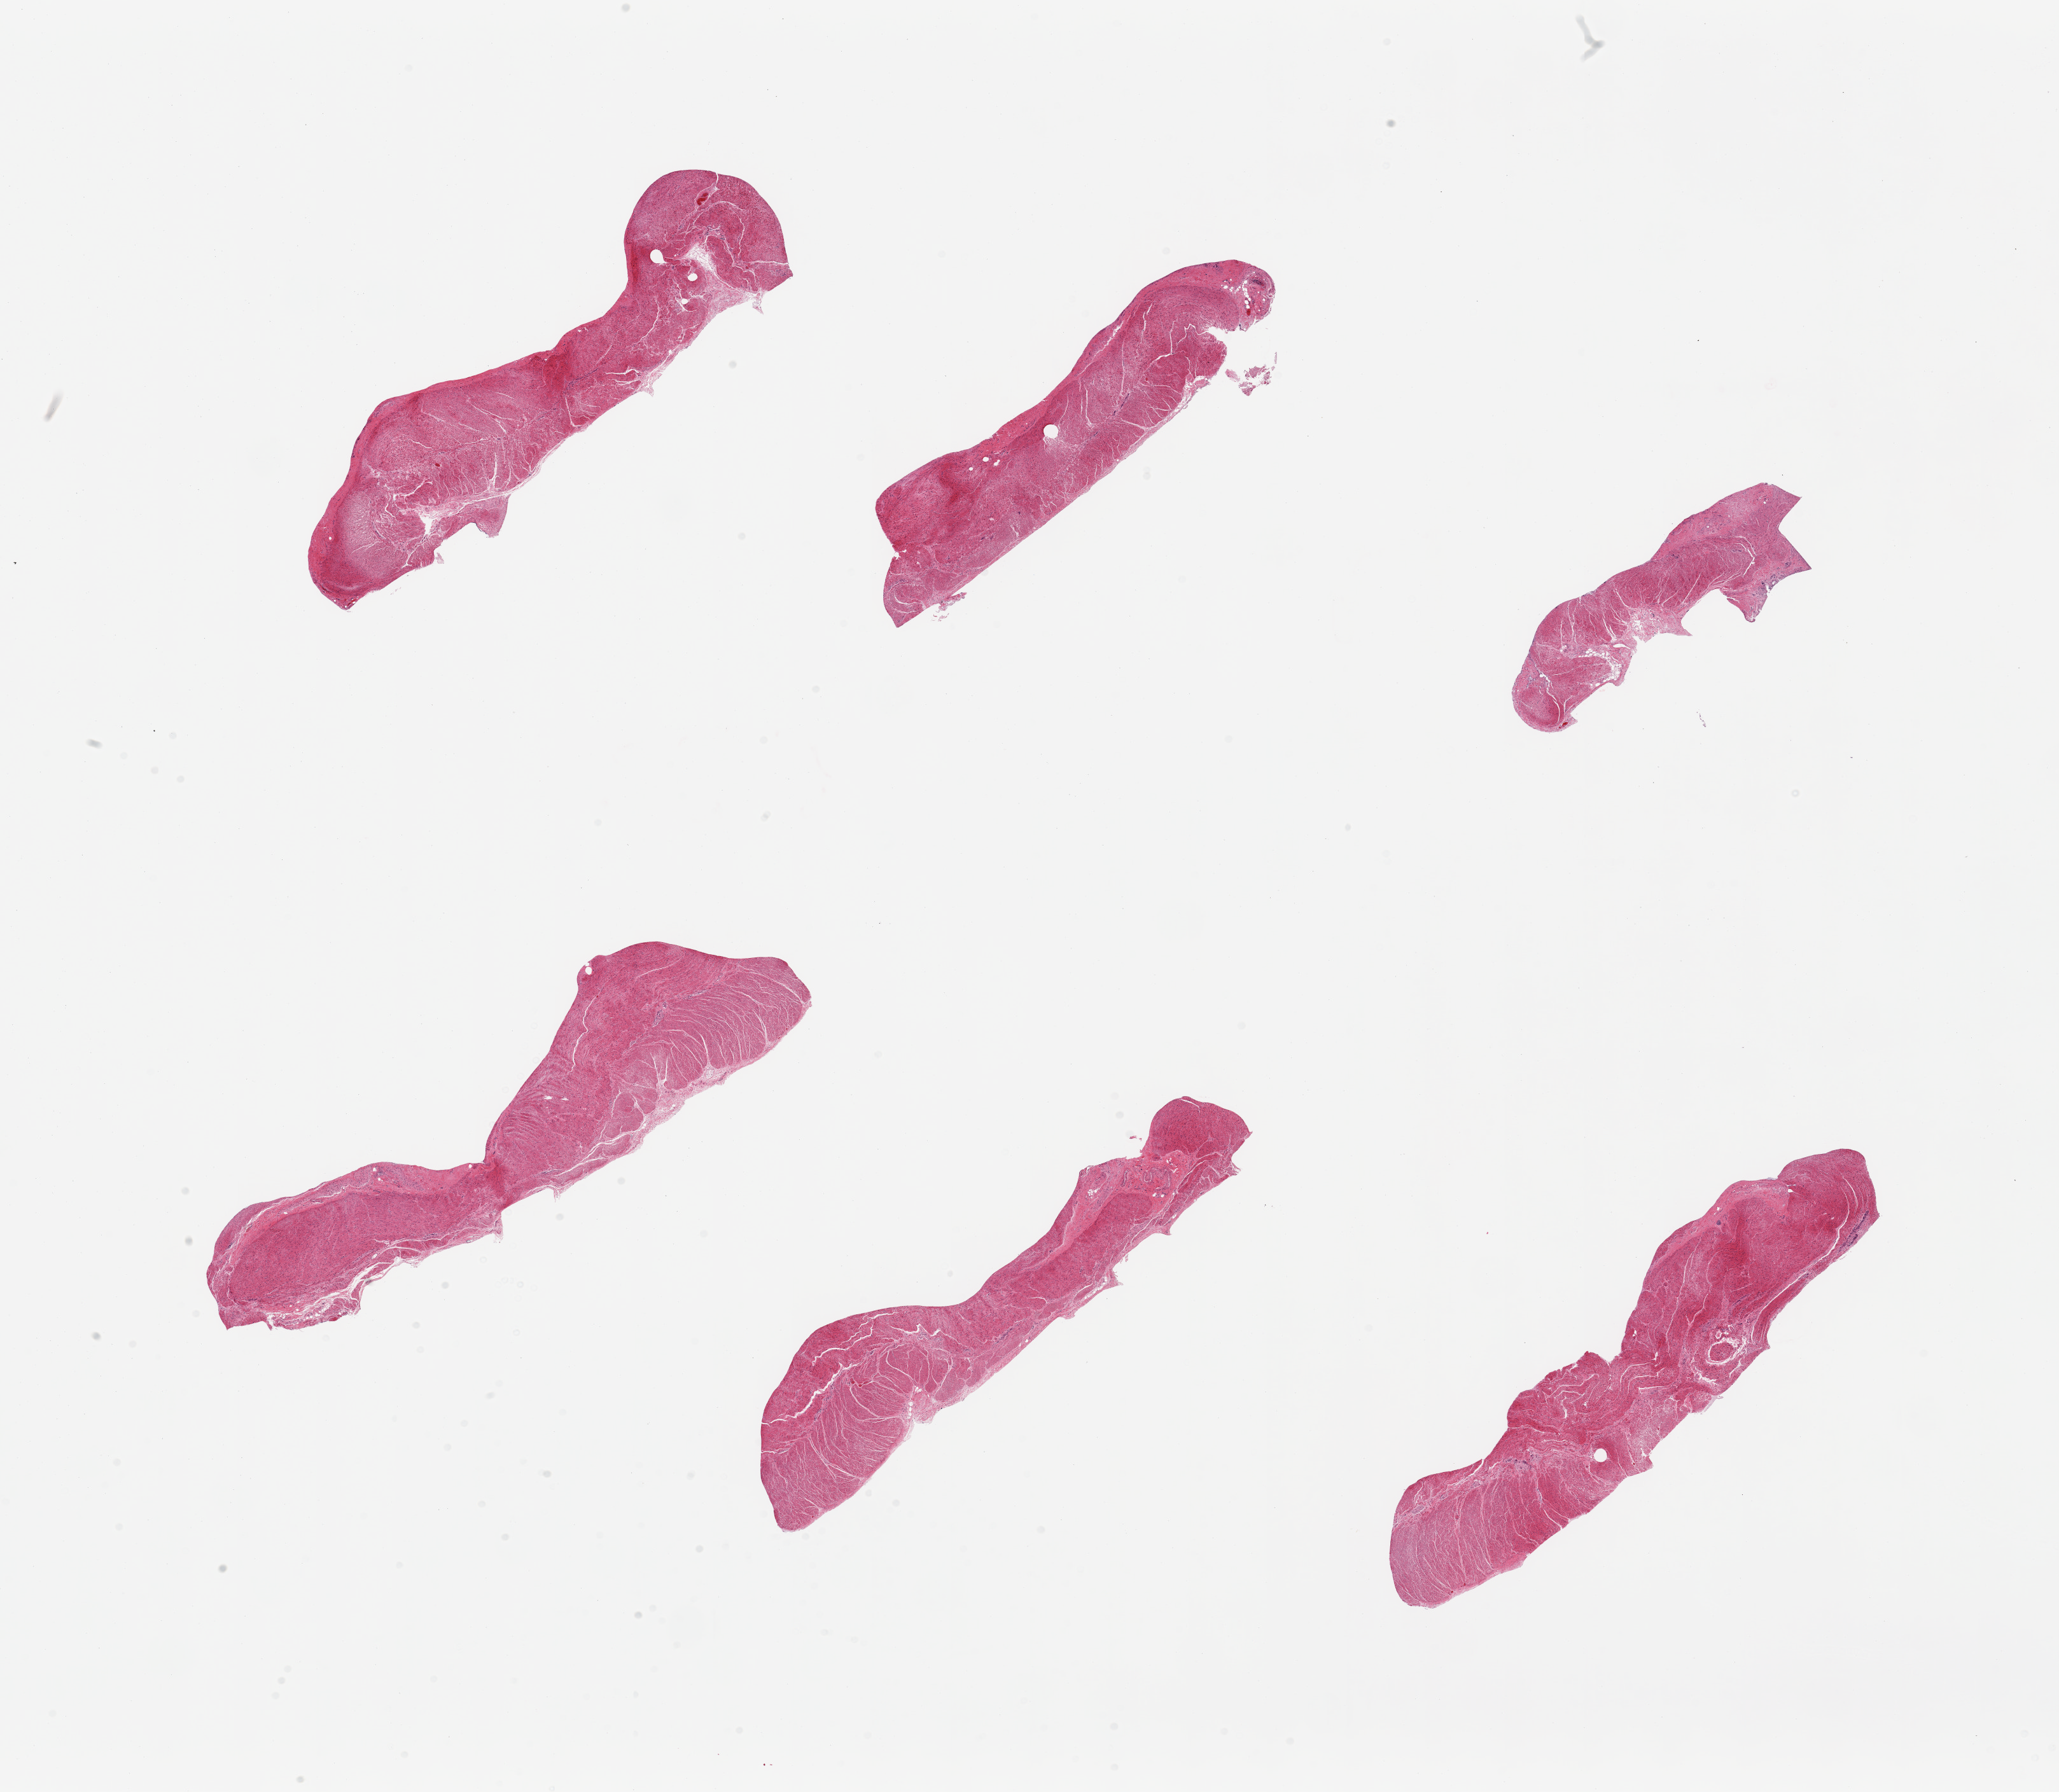
Whole-slide image, hematoxylin and eosin (H&E) stain, shown as a low-resolution overview of the whole scanned area (about 25.6 x 22.3 mm); PAXgene-fixed, paraffin-embedded tissue; section of sigmoid colon (target tissue); tissue donor sample. Donor sex: male.
Review note (as recorded): 6 pieces; well trimmed muscle.